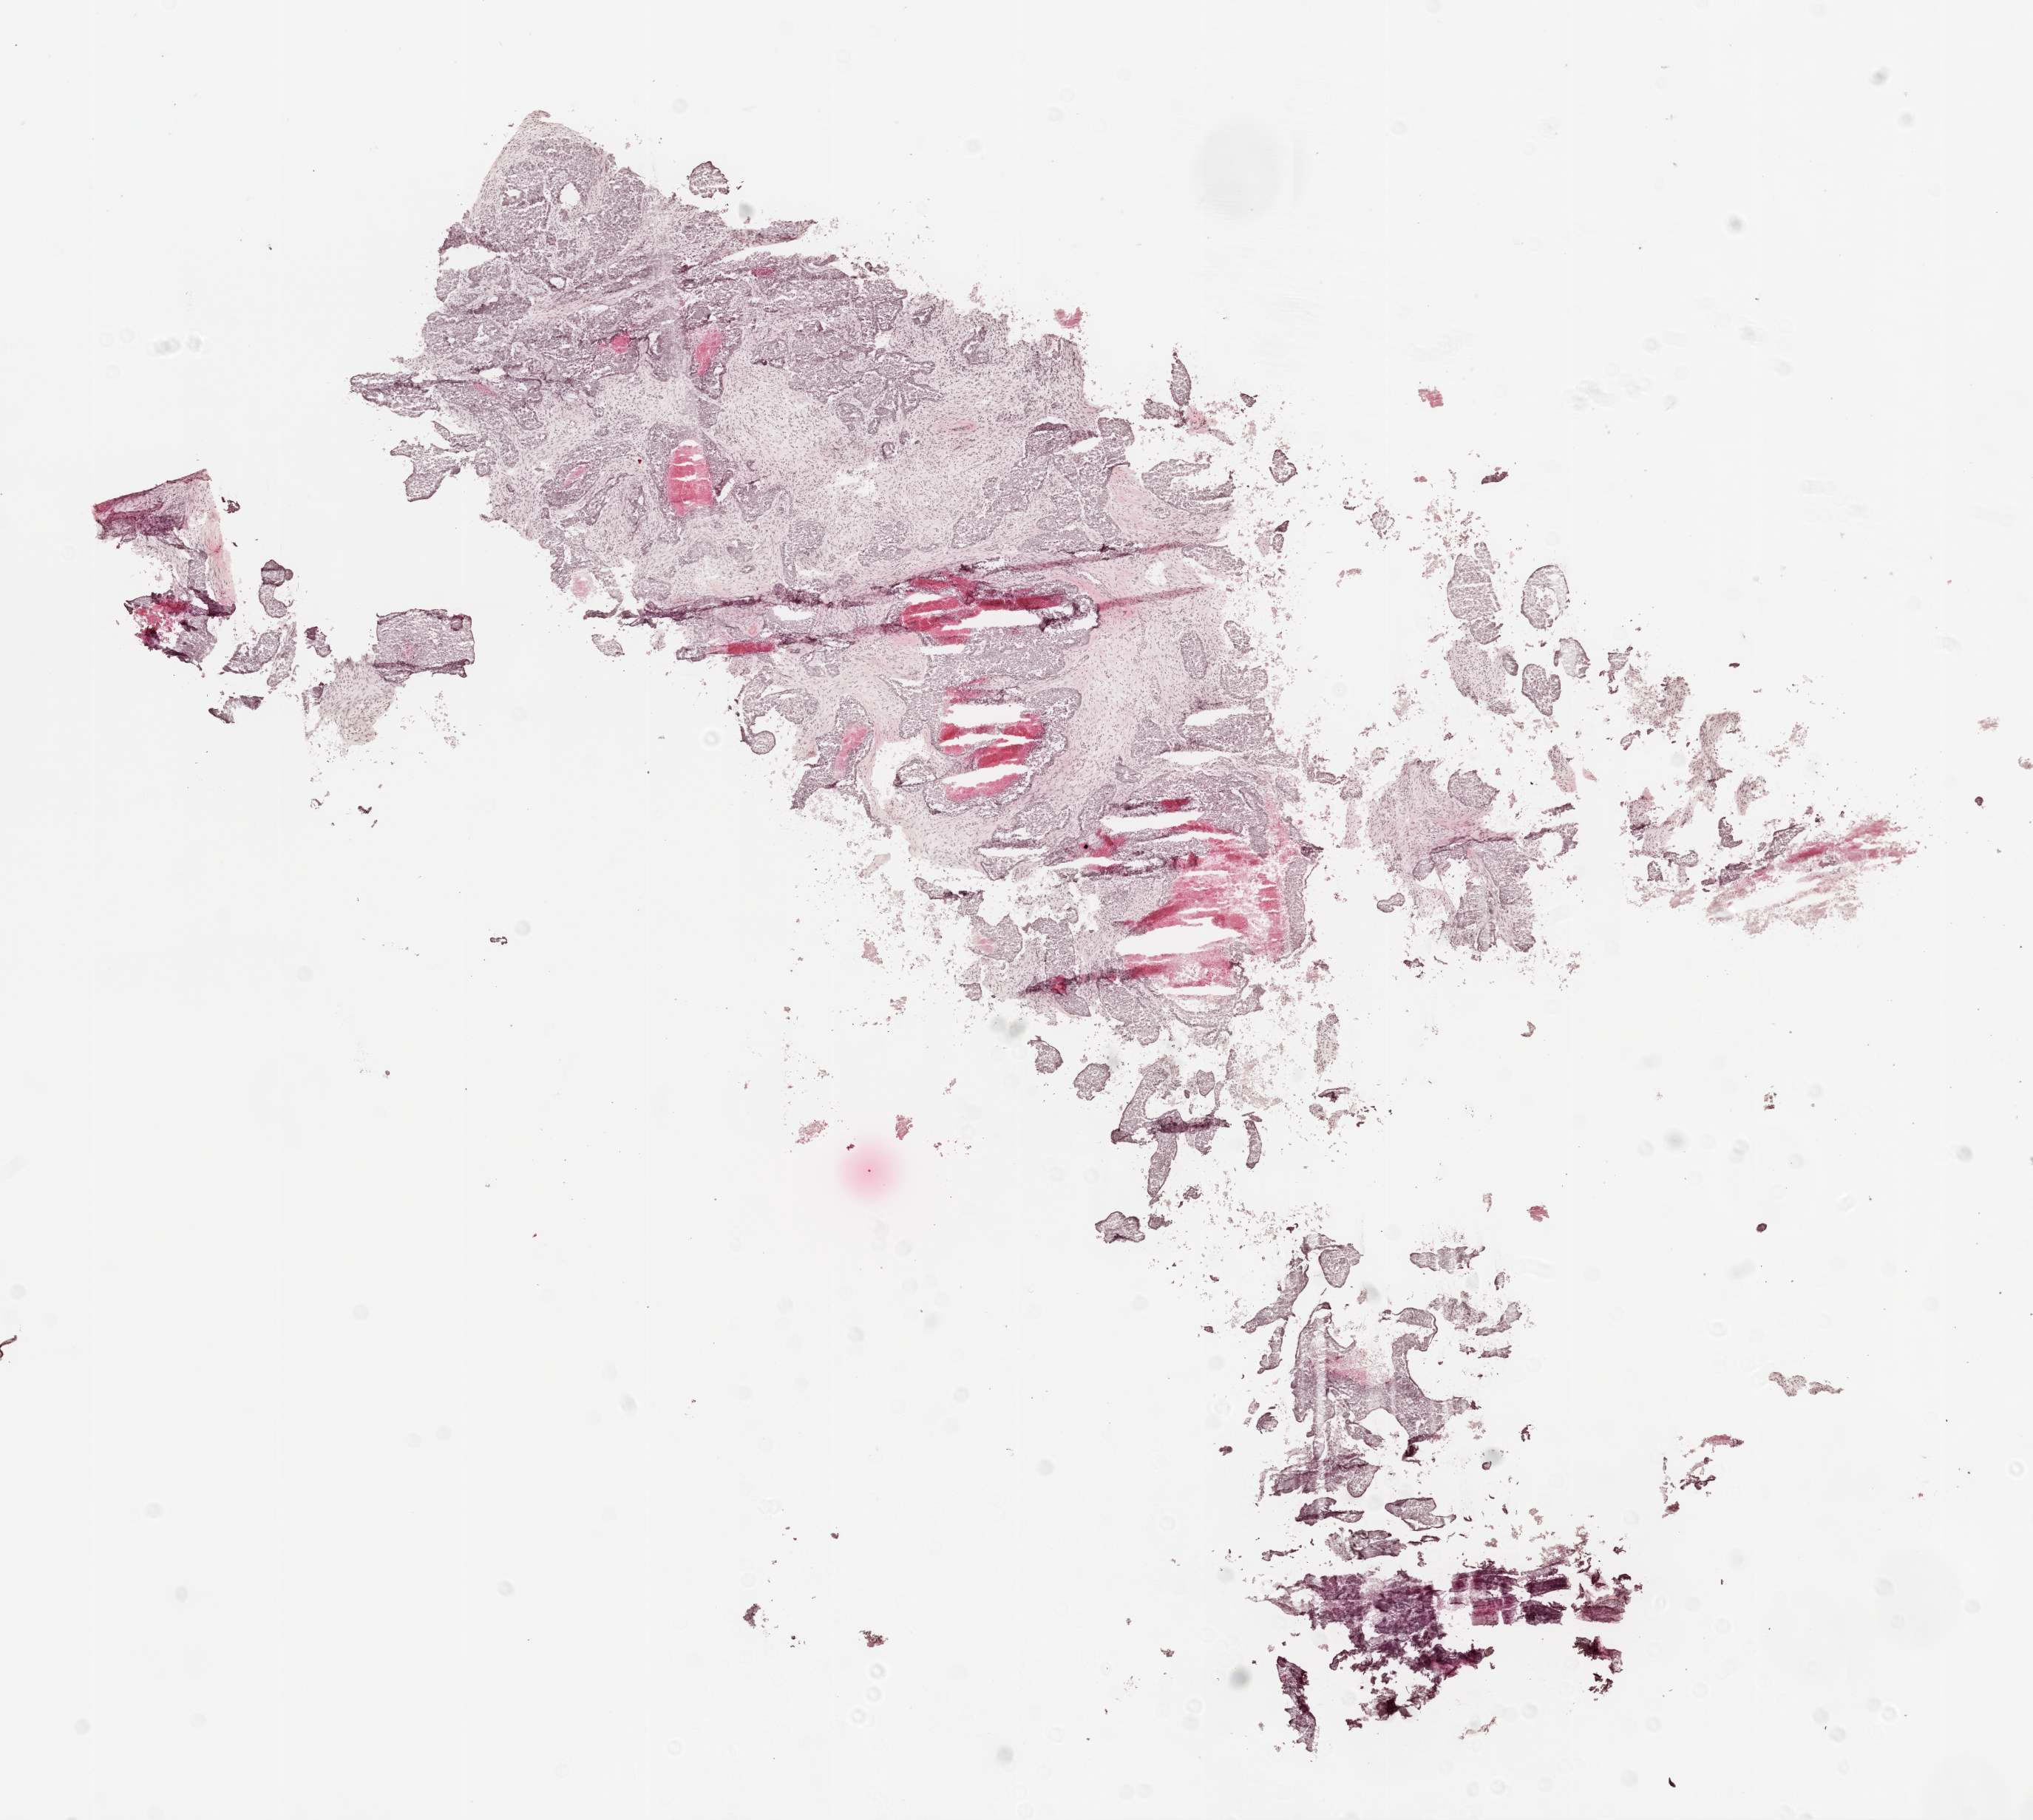
Whole-slide histology image, H&E-stained, shown as a low-resolution overview of the whole scanned area (about 11.0 x 9.9 mm), frozen section, sample: primary tumour, ovary. Female, age 61 years at initial diagnosis. Histologic grade: G2 (moderately differentiated). Pathologist review of this section (percent, as recorded): tumour cells 70%, tumour nuclei 80%, normal cells 0%, stromal cells 20%, necrosis 10%.
Diagnosis: Serous cystadenocarcinoma, NOS. FIGO stage: IIIC.